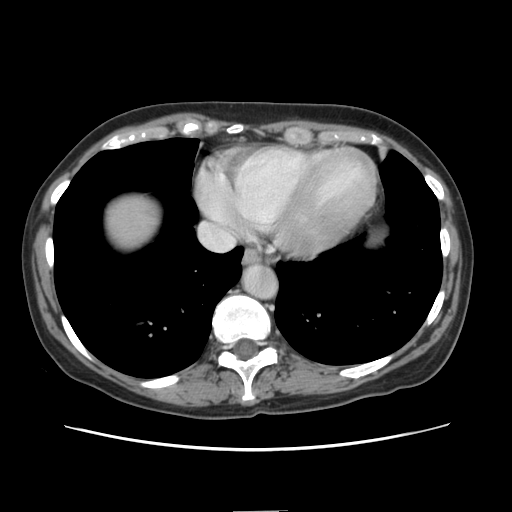
Contrast-enhanced abdominal CT, one axial slice. Position 133 of 141 along the scan axis. 120 kVp. Intravenous contrast given. Soft-tissue window (W 400 / L 40 HU). 2.5 mm slice thickness. 512 × 512 image matrix. Female patient, age 63 years. Case-level facts recorded for this patient, not image findings: diagnosis: colorectal cancer liver metastases, imaged before liver resection.
Structures marked on this image (expert manual segmentation):
- liver: bounding box [x1, y1, x2, y2] px = [104, 195, 159, 253]